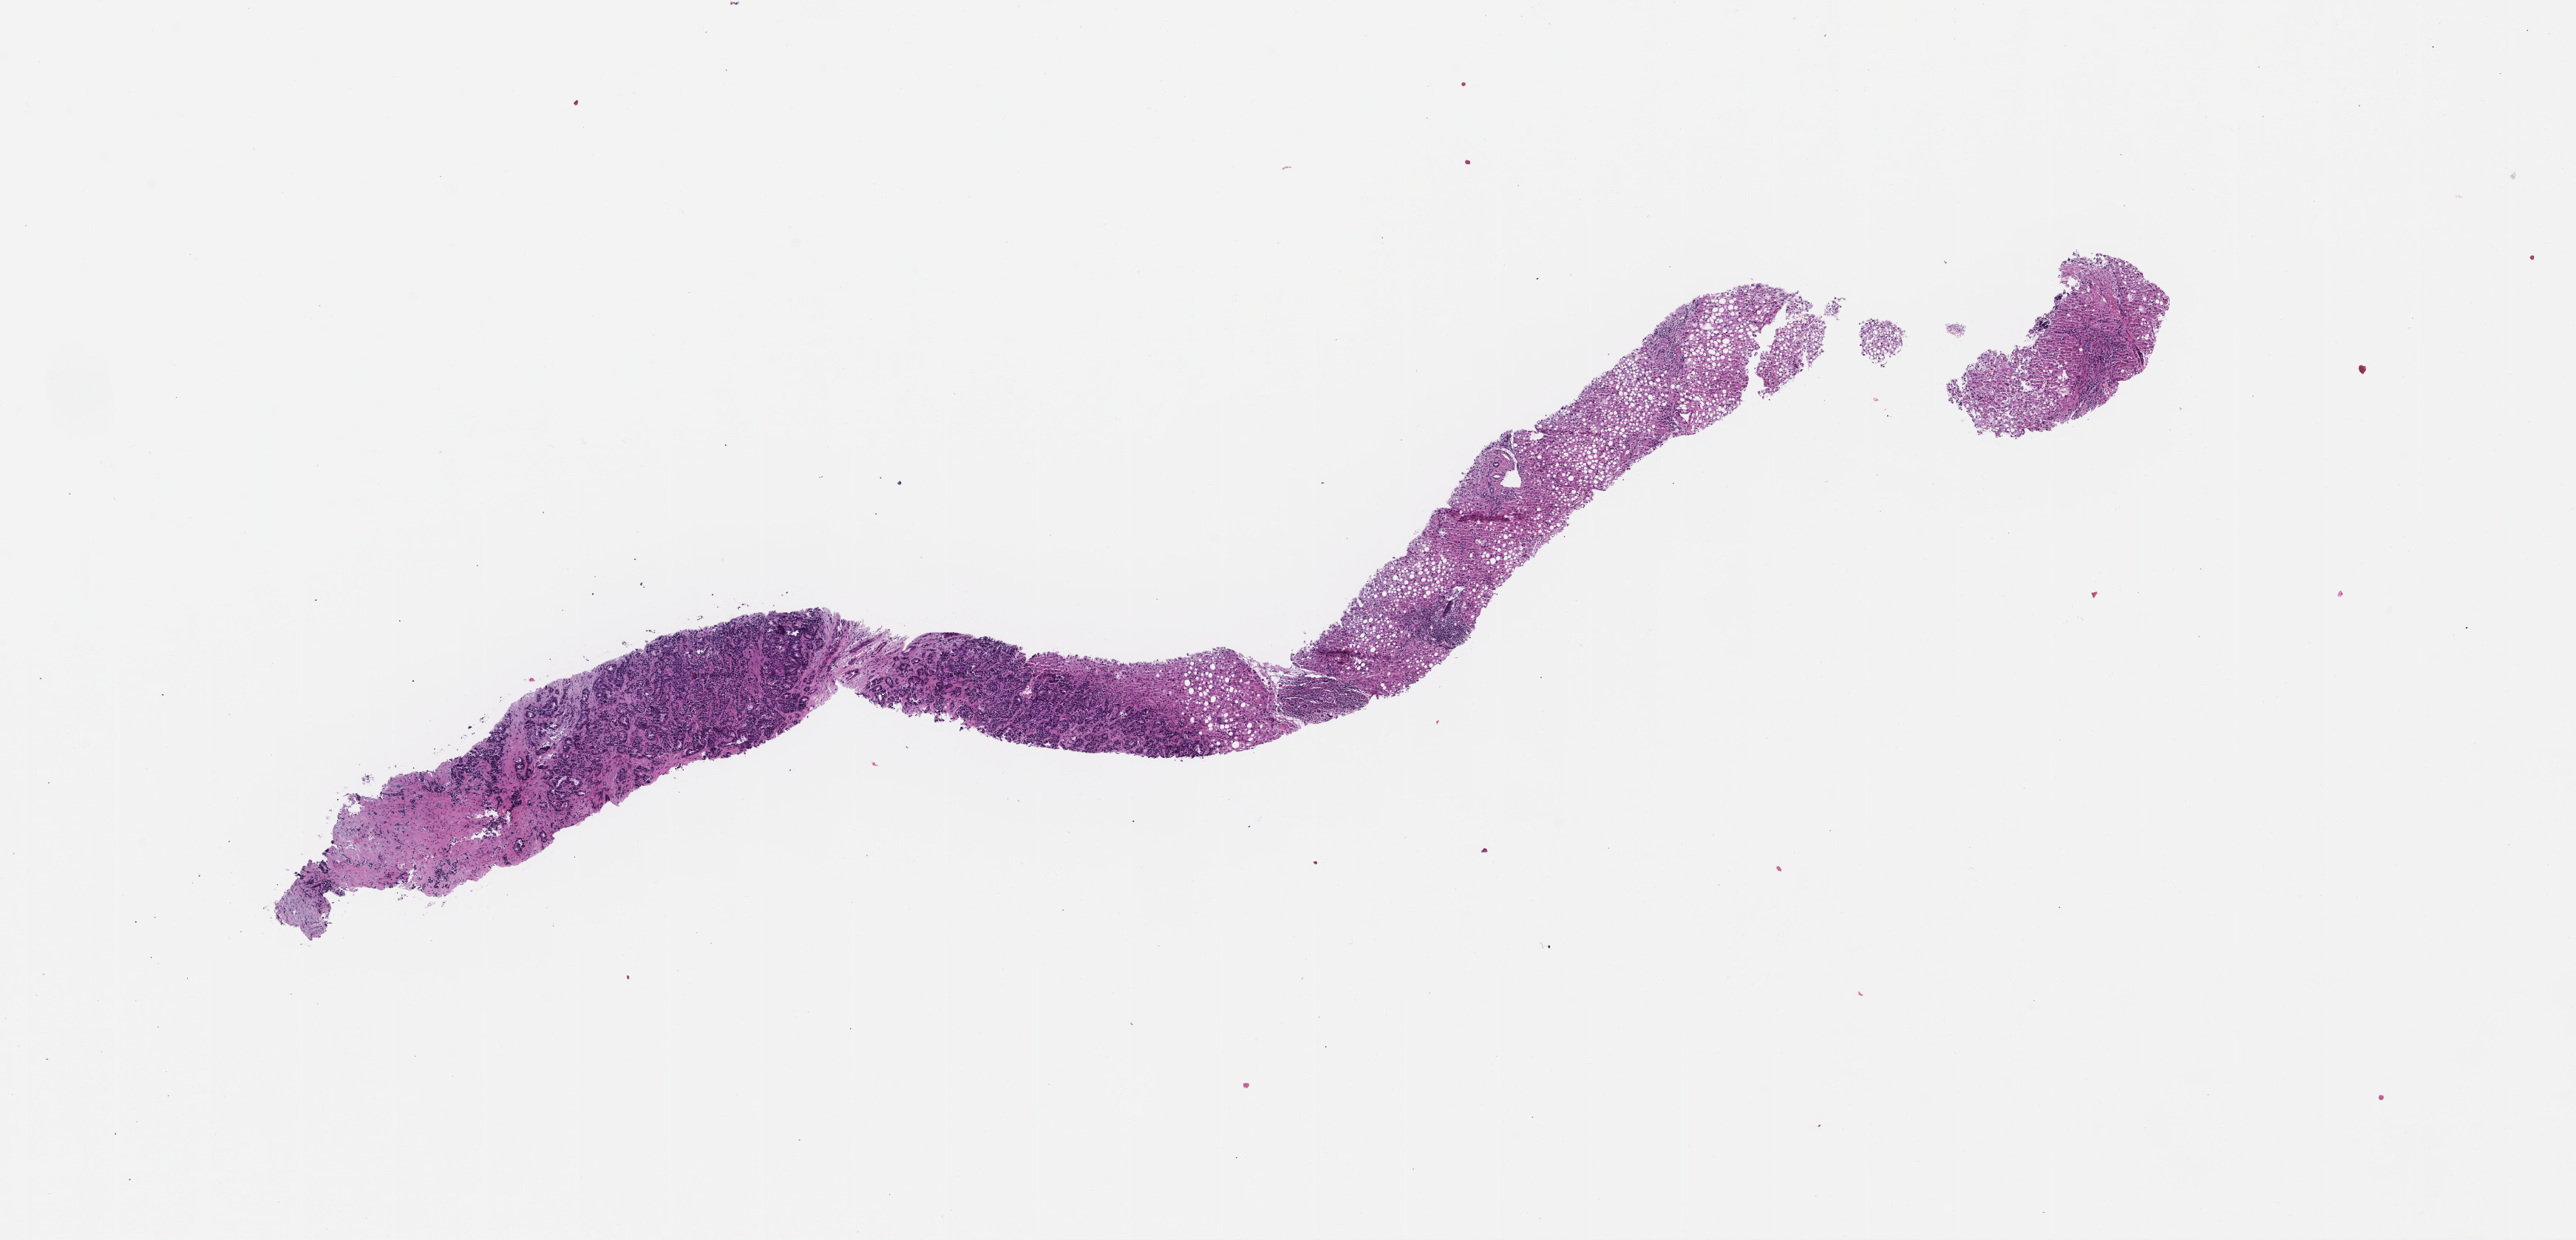
Whole-slide image, hematoxylin and eosin (H&E) stain, a low-resolution overview of the entire scanned area, about 14.1 x 6.8 mm, formalin-fixed, paraffin-embedded (FFPE) tissue, site: colon, specimen time point: collected at baseline (before treatment). Patient sex: female.
This section: primary tumour tissue. Diagnosis: Colorectal Carcinoma.